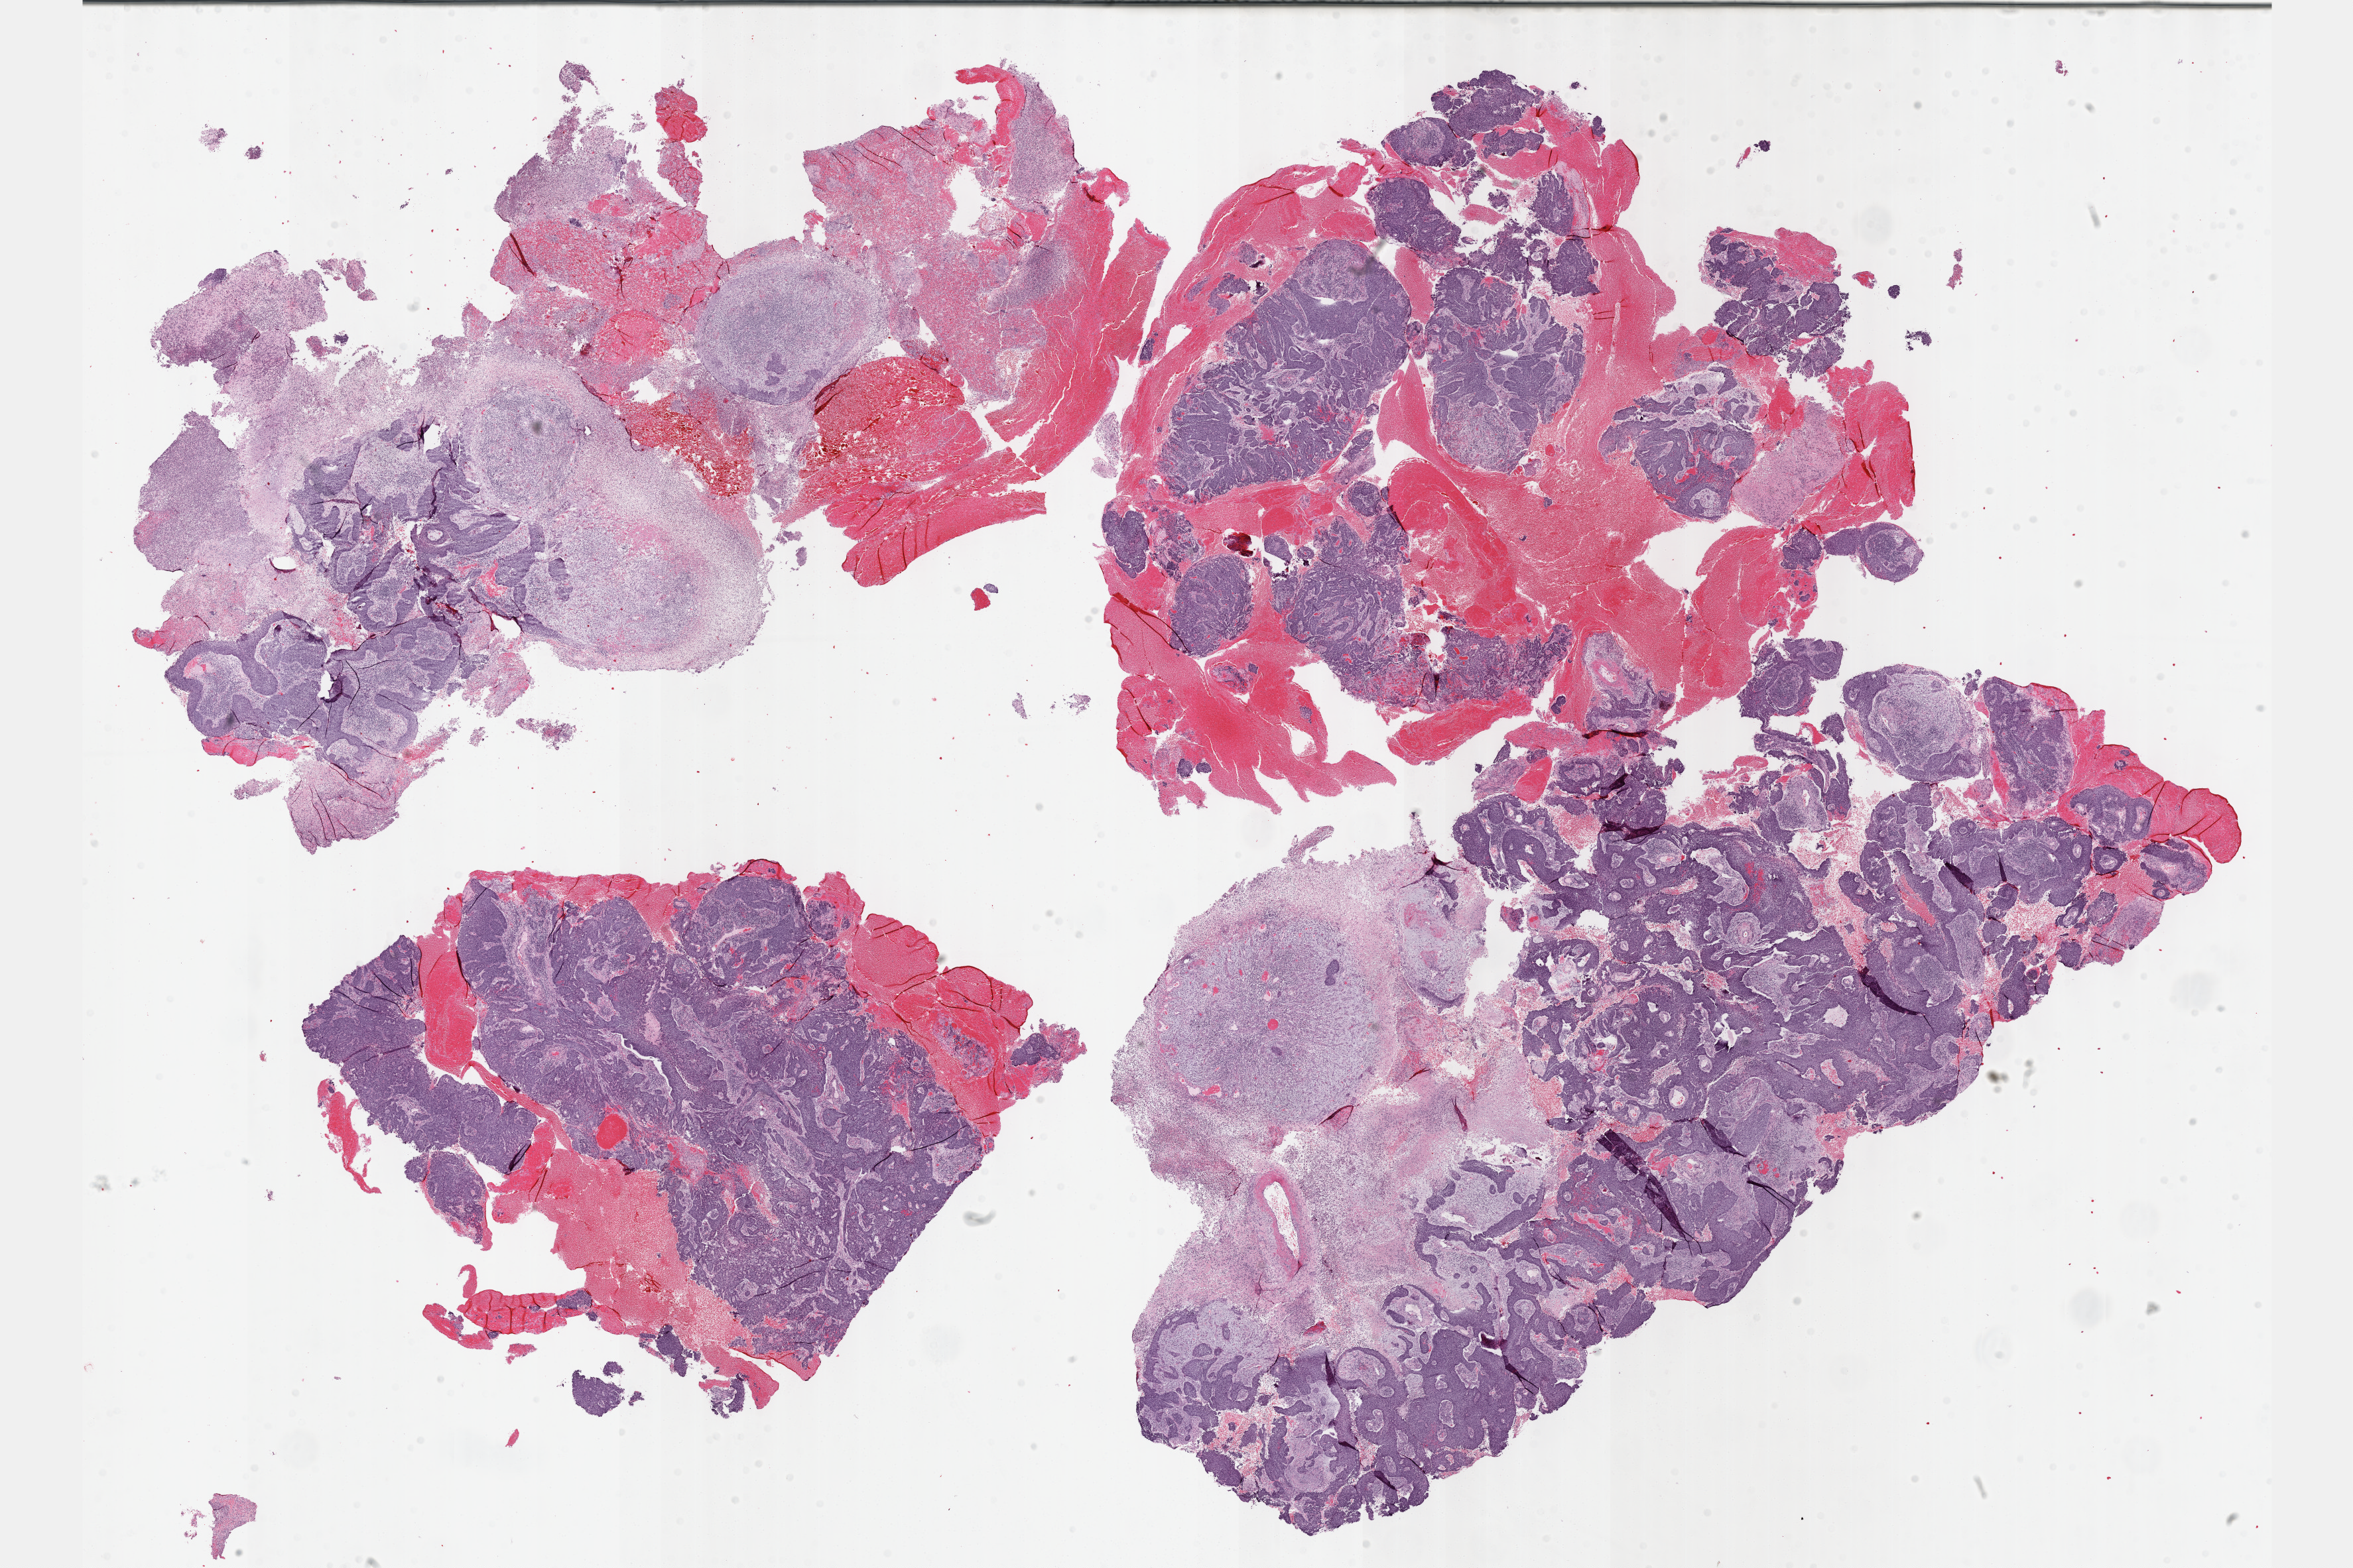
H&E whole-slide image — whole scanned area (about 28.7 x 19.1 mm, slide scanned at 40x) shown as a low-resolution overview, FFPE section, cervix, primary tumour sample. Female patient; age at initial diagnosis 46 years. Histologic grade: GX (grade cannot be assessed).
* FIGO stage: I
* diagnosis: Squamous cell carcinoma, keratinizing, NOS